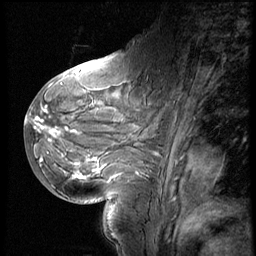
Breast MRI (dynamic contrast-enhanced), one sagittal slice. Slice 25 of 60 in the series (ordered by position). 3 images stored at this slice position (order not interpretable as contrast timing). 1.5 T. TE 4.2 ms, TR 8.9 ms. 2.5 mm slice thickness. 256 × 256 image matrix, field of view 200 × 200 mm. Patient: female, 29 years. Case-level facts recorded for this patient, not image findings: setting: breast cancer imaged before/during neoadjuvant chemotherapy.
Outlined on this slice (semi-automatic segmentation, software-assisted and operator-edited):
- analysis volume of interest (the breast-tissue region the enhancement analysis was run in; not a lesion): bounding box (x1, y1, x2, y2) in pixels: (29, 57, 173, 200)
- tumour enhancement mask (voxels above the 140 % enhancement threshold inside the analysis volume of interest): (34, 108, 102, 180)